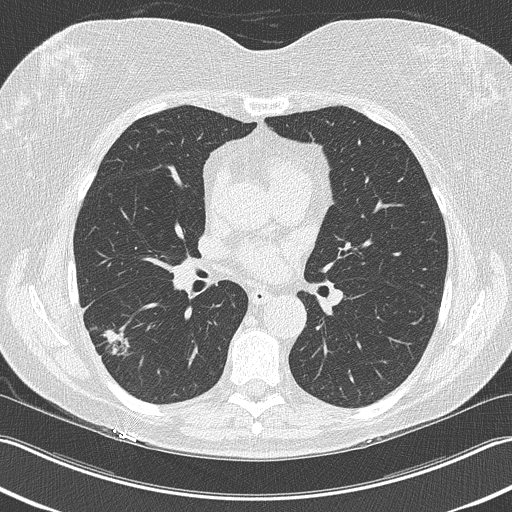
Low-dose screening chest CT, one axial slice; position 121 of 210 along the scan axis; reconstruction kernel B50f; 120 kVp; lung window (W 1500 / L -600 HU); 512 × 512 image matrix, field of view 348 × 348 mm.
Outlined on this slice (expert manual segmentation):
- lesion 1 (tumor, lower lobe of right lung): bounding box (x1, y1, x2, y2) in pixels: (100, 329, 131, 356)